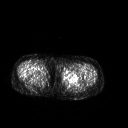
FDG PET of an extremity soft-tissue mass (from a PET/CT study), one axial slice; position 227 of 267 along the scan axis; 3.27 mm slice thickness; 128 × 128 image matrix. Female patient, age 42 years. Case-level facts recorded for this patient, not image findings: histological type: pleiomorphic leiomyosarcoma; grade: intermediate; site of the primary tumour: left thigh.
Outlined on this slice (expert contour drawn on MRI and transferred to this co-registered scan by the dataset authors):
- gross tumour volume including surrounding oedema: bounding box [x1, y1, x2, y2] px = [62, 69, 82, 81]
- gross tumour volume (mass): [62, 69, 78, 81]